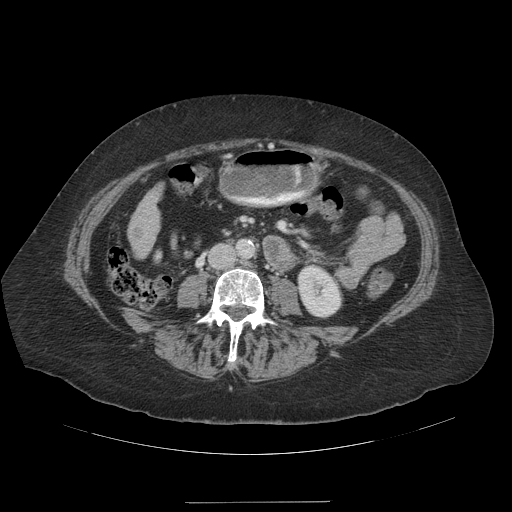
Contrast-enhanced abdominal CT (liver protocol), one axial slice; slice 29 of 99 in the series (ordered by position); 140 kVp; soft-tissue window (W 400 / L 40 HU); 2.5 mm slice thickness; 512 × 512 image matrix, field of view 440 × 440 mm. Case-level facts recorded for this patient, not image findings: diagnosis: hepatocellular carcinoma (patient treated with transarterial chemoembolisation; whether this scan precedes or follows treatment is not stated here); TNM stage (as recorded): Stage-IVA; Child-Pugh class: A; tumour nodularity: multinodular.
Structures marked on this image (semi-automatic segmentation, software-assisted and operator-edited):
- liver parenchyma outside the tumour (the mass and vessels are separate outlines, so this box may not span the whole liver): bounding box (x1, y1, x2, y2) in pixels: (128, 186, 162, 258)